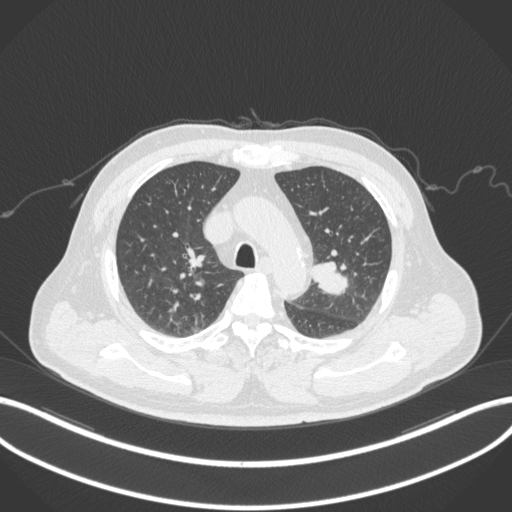
Chest CT, one axial slice. Position 220 of 286 along the scan axis. Reconstruction kernel B31f. Lung window (W 1500 / L -600 HU). 1 mm slice thickness. 512 × 512 image matrix, field of view 400 × 400 mm. Patient: male, 67 years. Case-level facts recorded for this patient, not image findings: clinical TNM (as recorded): T2a N1 M0; histopathological grade: G3.
Outlined on this slice (rectangle marked by the reading radiologist):
- lung tumour (recorded histology: adenocarcinoma): bounding box <309,256,348,300> (left, top, right, bottom; pixels)